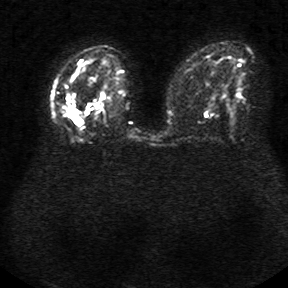
Breast MRI, one axial slice; position 15 of 34 along the scan axis; diffusion-weighted series; image 2 of 4 stored at this slice position (different b-values; order by instance number); 1.5 T; 5 mm slice thickness; 288 × 288 image matrix, field of view 340 × 340 mm. Female patient.
Structures marked on this image (manually delineated by an expert):
- tumour on diffusion-weighted imaging: bounding box [x1, y1, x2, y2] px = [85, 91, 105, 115]